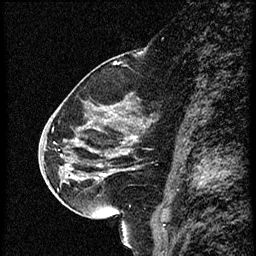
Breast MRI (dynamic contrast-enhanced), one sagittal slice; dynamic contrast-enhanced study with each time point stored as its own series, time point 2 of 4 at this slice position (early post-contrast, ordered by acquisition time); 1.5 T; TE 4.2 ms, TR 18.9 ms; 2 mm slice thickness; 256 × 256 image matrix. Female patient. From the clinical record (not read from this slice): setting: breast cancer imaged before/during neoadjuvant chemotherapy; receptor status: HER2-positive.
Outlined on this slice (semi-automatic segmentation, software-assisted and operator-edited):
- analysis volume of interest (the breast-tissue region the enhancement analysis was run in; not a lesion): bounding box (x1, y1, x2, y2) in pixels: (63, 80, 163, 215)
- tumour enhancement mask (voxels above the 100 % enhancement threshold inside the analysis volume of interest): (98, 138, 136, 179)